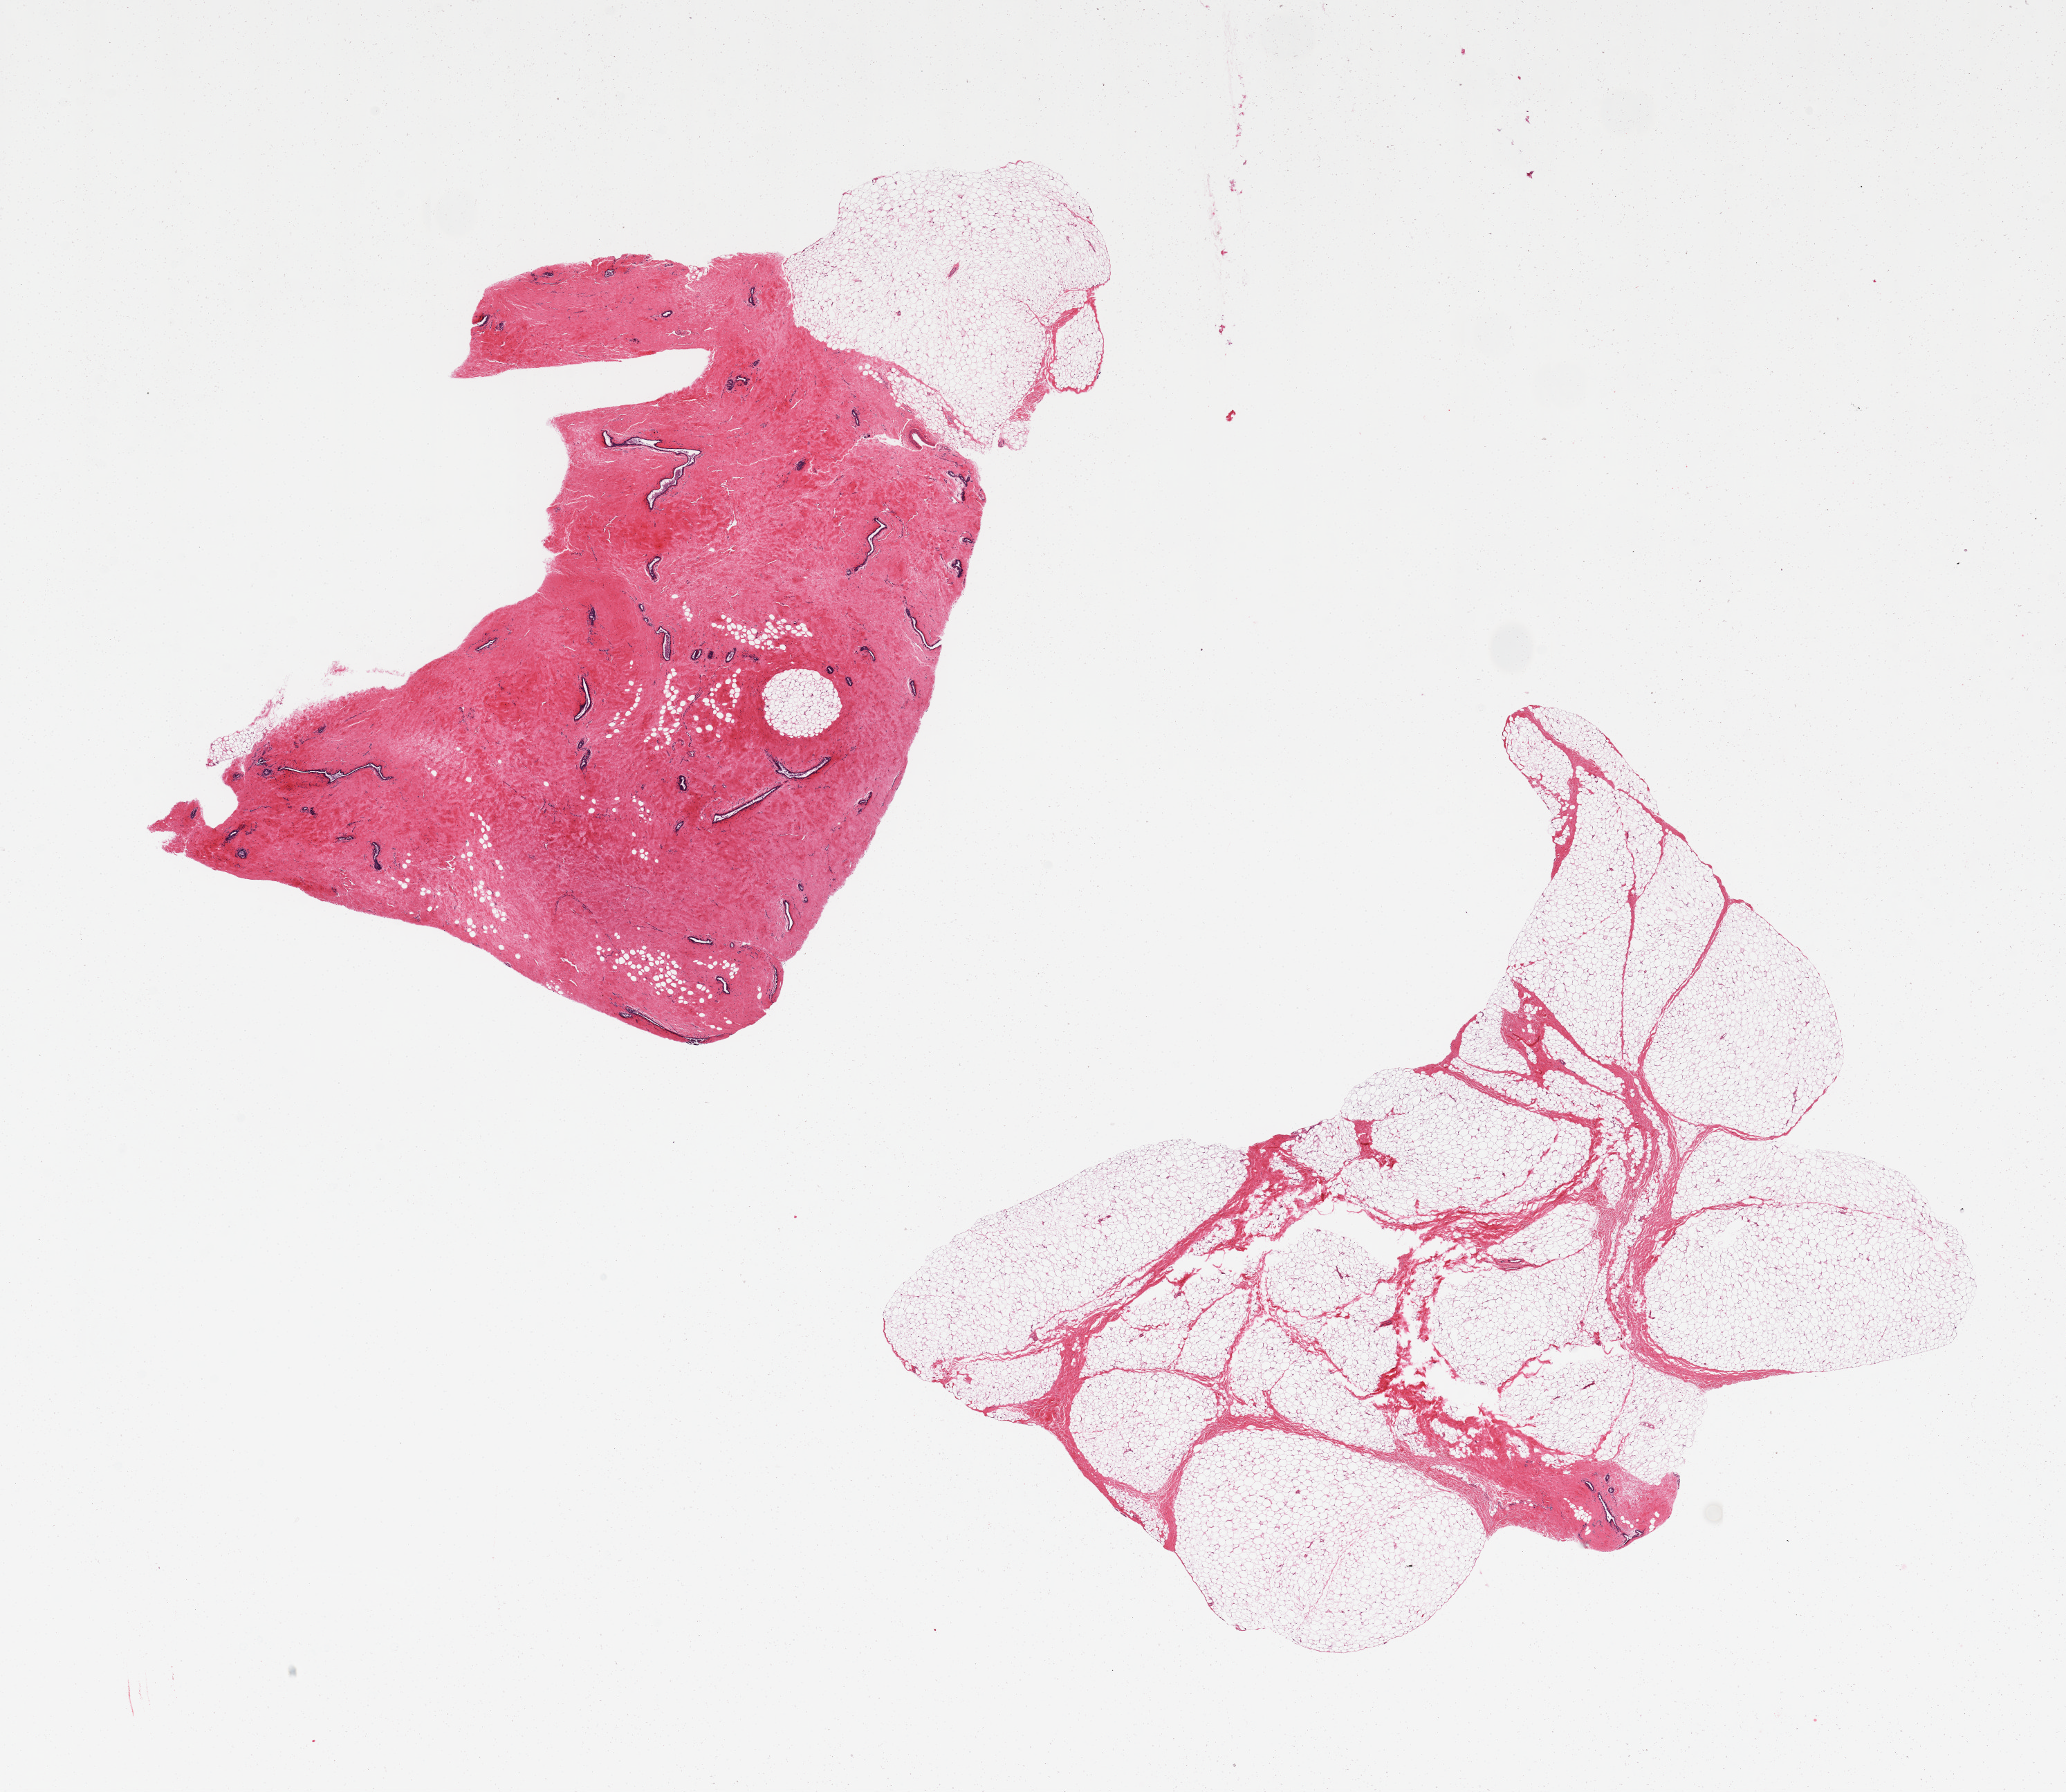
Whole-slide image, hematoxylin and eosin (H&E) stain, a low-resolution overview of the entire scanned area, about 23.6 x 20.5 mm. PAXgene-fixed, paraffin-embedded tissue. Target tissue: breast. Tissue donor sample. Donor: male.
Pathologist's review note for this sample: 2 pieces, 1 with gynecomastoid changes:fibrosis and ducts; other largely fat with focus of ducts.